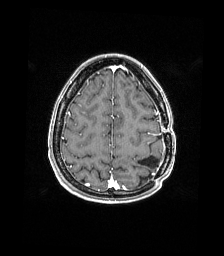
Brain MRI from a brain-tumour surgery series, one axial slice; position 48 of 176 along the scan axis; T1-weighted post-contrast; 1 mm slice thickness; 224 × 256 image matrix, field of view 224 × 256 mm. From the clinical record (not read from this slice): histopathology: Atypical meningioma; WHO grade: 2; tumour location: Paramedian Left Parietal.
Structures marked on this image (manually delineated by an expert):
- previous resection cavity: bounding box <139,156,159,169> (left, top, right, bottom; pixels)